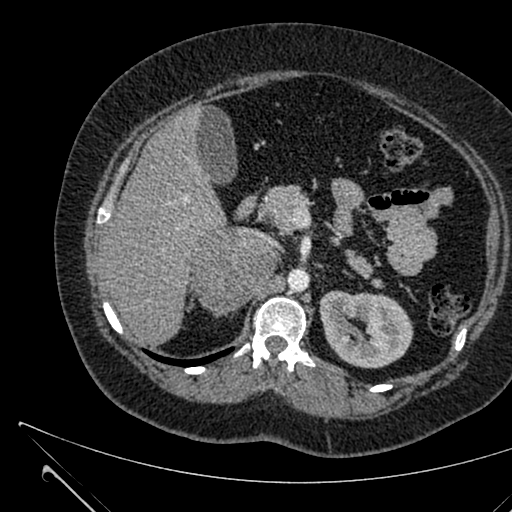
Contrast-enhanced abdominal CT, one axial slice. Position 406 of 731 along the scan axis. 120 kVp. Intravenous contrast given. Soft-tissue window (W 400 / L 40 HU). 512 × 512 image matrix. Patient: female, 36 years. Case-level facts recorded for this patient, not image findings: diagnosis: adrenocortical carcinoma; tumour side: right adrenal; tumour size at pathology: 10 cm; Ki-67 index: 20 %; stage (as recorded): 4.
Annotated regions visible in this slice (semi-automatically segmented with operator editing):
- mass: bounding box (x1, y1, x2, y2) in pixels: (194, 228, 275, 314)